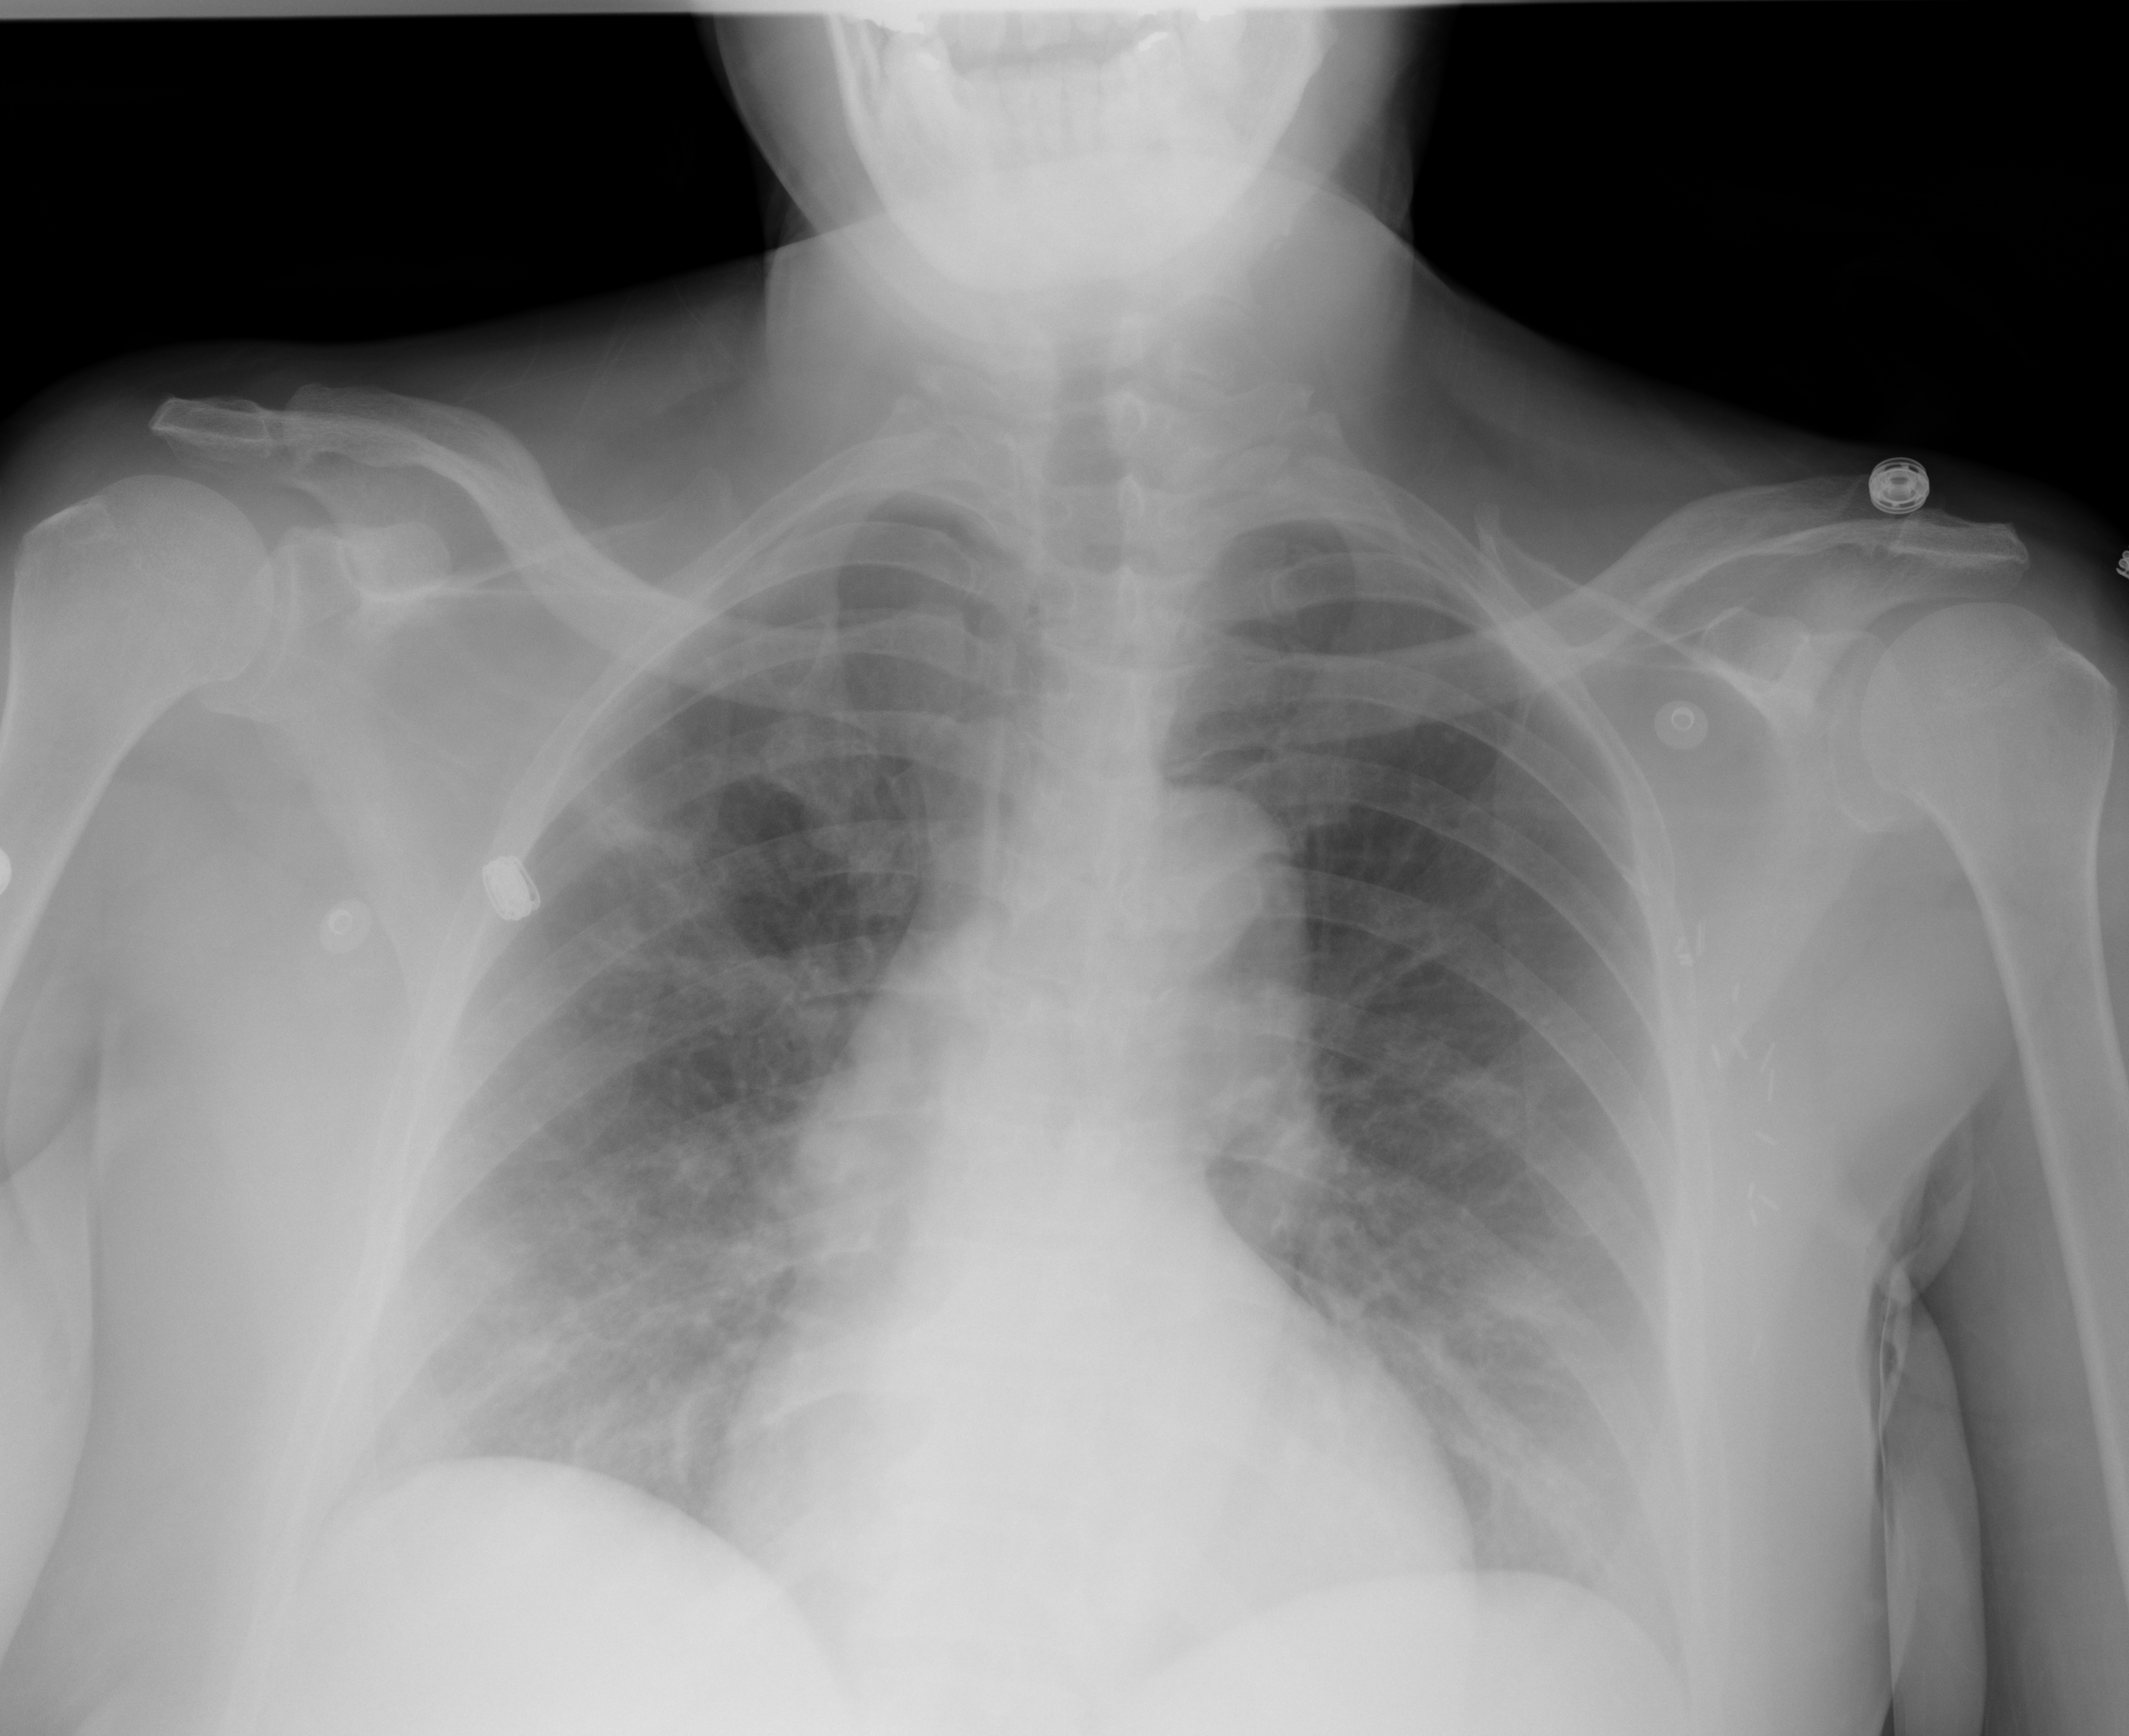
Portable chest radiograph, AP projection. Female patient, age 55 years; imaged 0 days after the COVID-19 diagnosis.
Radiologist's key findings for this exam: subtle peribronchovascular opacities are noted within both lung bases. There is somewhat bandlike opacity seen in the region of the lateral right upper lung.